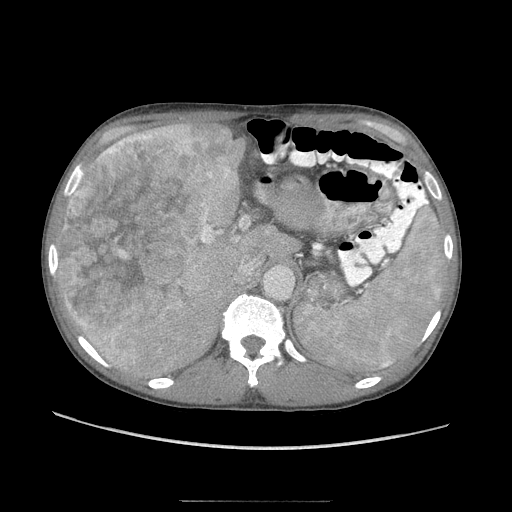
Contrast-enhanced abdominal CT (liver protocol), one axial slice. Slice 63 of 103 in the series (ordered by position). Soft-tissue window (W 400 / L 40 HU). 512 × 512 image matrix, field of view 380 × 380 mm. From the clinical record (not read from this slice): diagnosis: hepatocellular carcinoma (patient treated with transarterial chemoembolisation; whether this scan precedes or follows treatment is not stated here); TNM stage (as recorded): Stage-IIIA; Child-Pugh class: A; tumour nodularity: multinodular; tumour size: 16 cm.
Annotated regions visible in this slice (semi-automatic segmentation, software-assisted and operator-edited):
- liver parenchyma outside the tumour (the mass and vessels are separate outlines, so this box may not span the whole liver): box from (x=56, y=116) to (x=282, y=378) px
- mass: (x=55, y=123)–(x=236, y=369)
- liver vessels: (x=107, y=228)–(x=222, y=367)